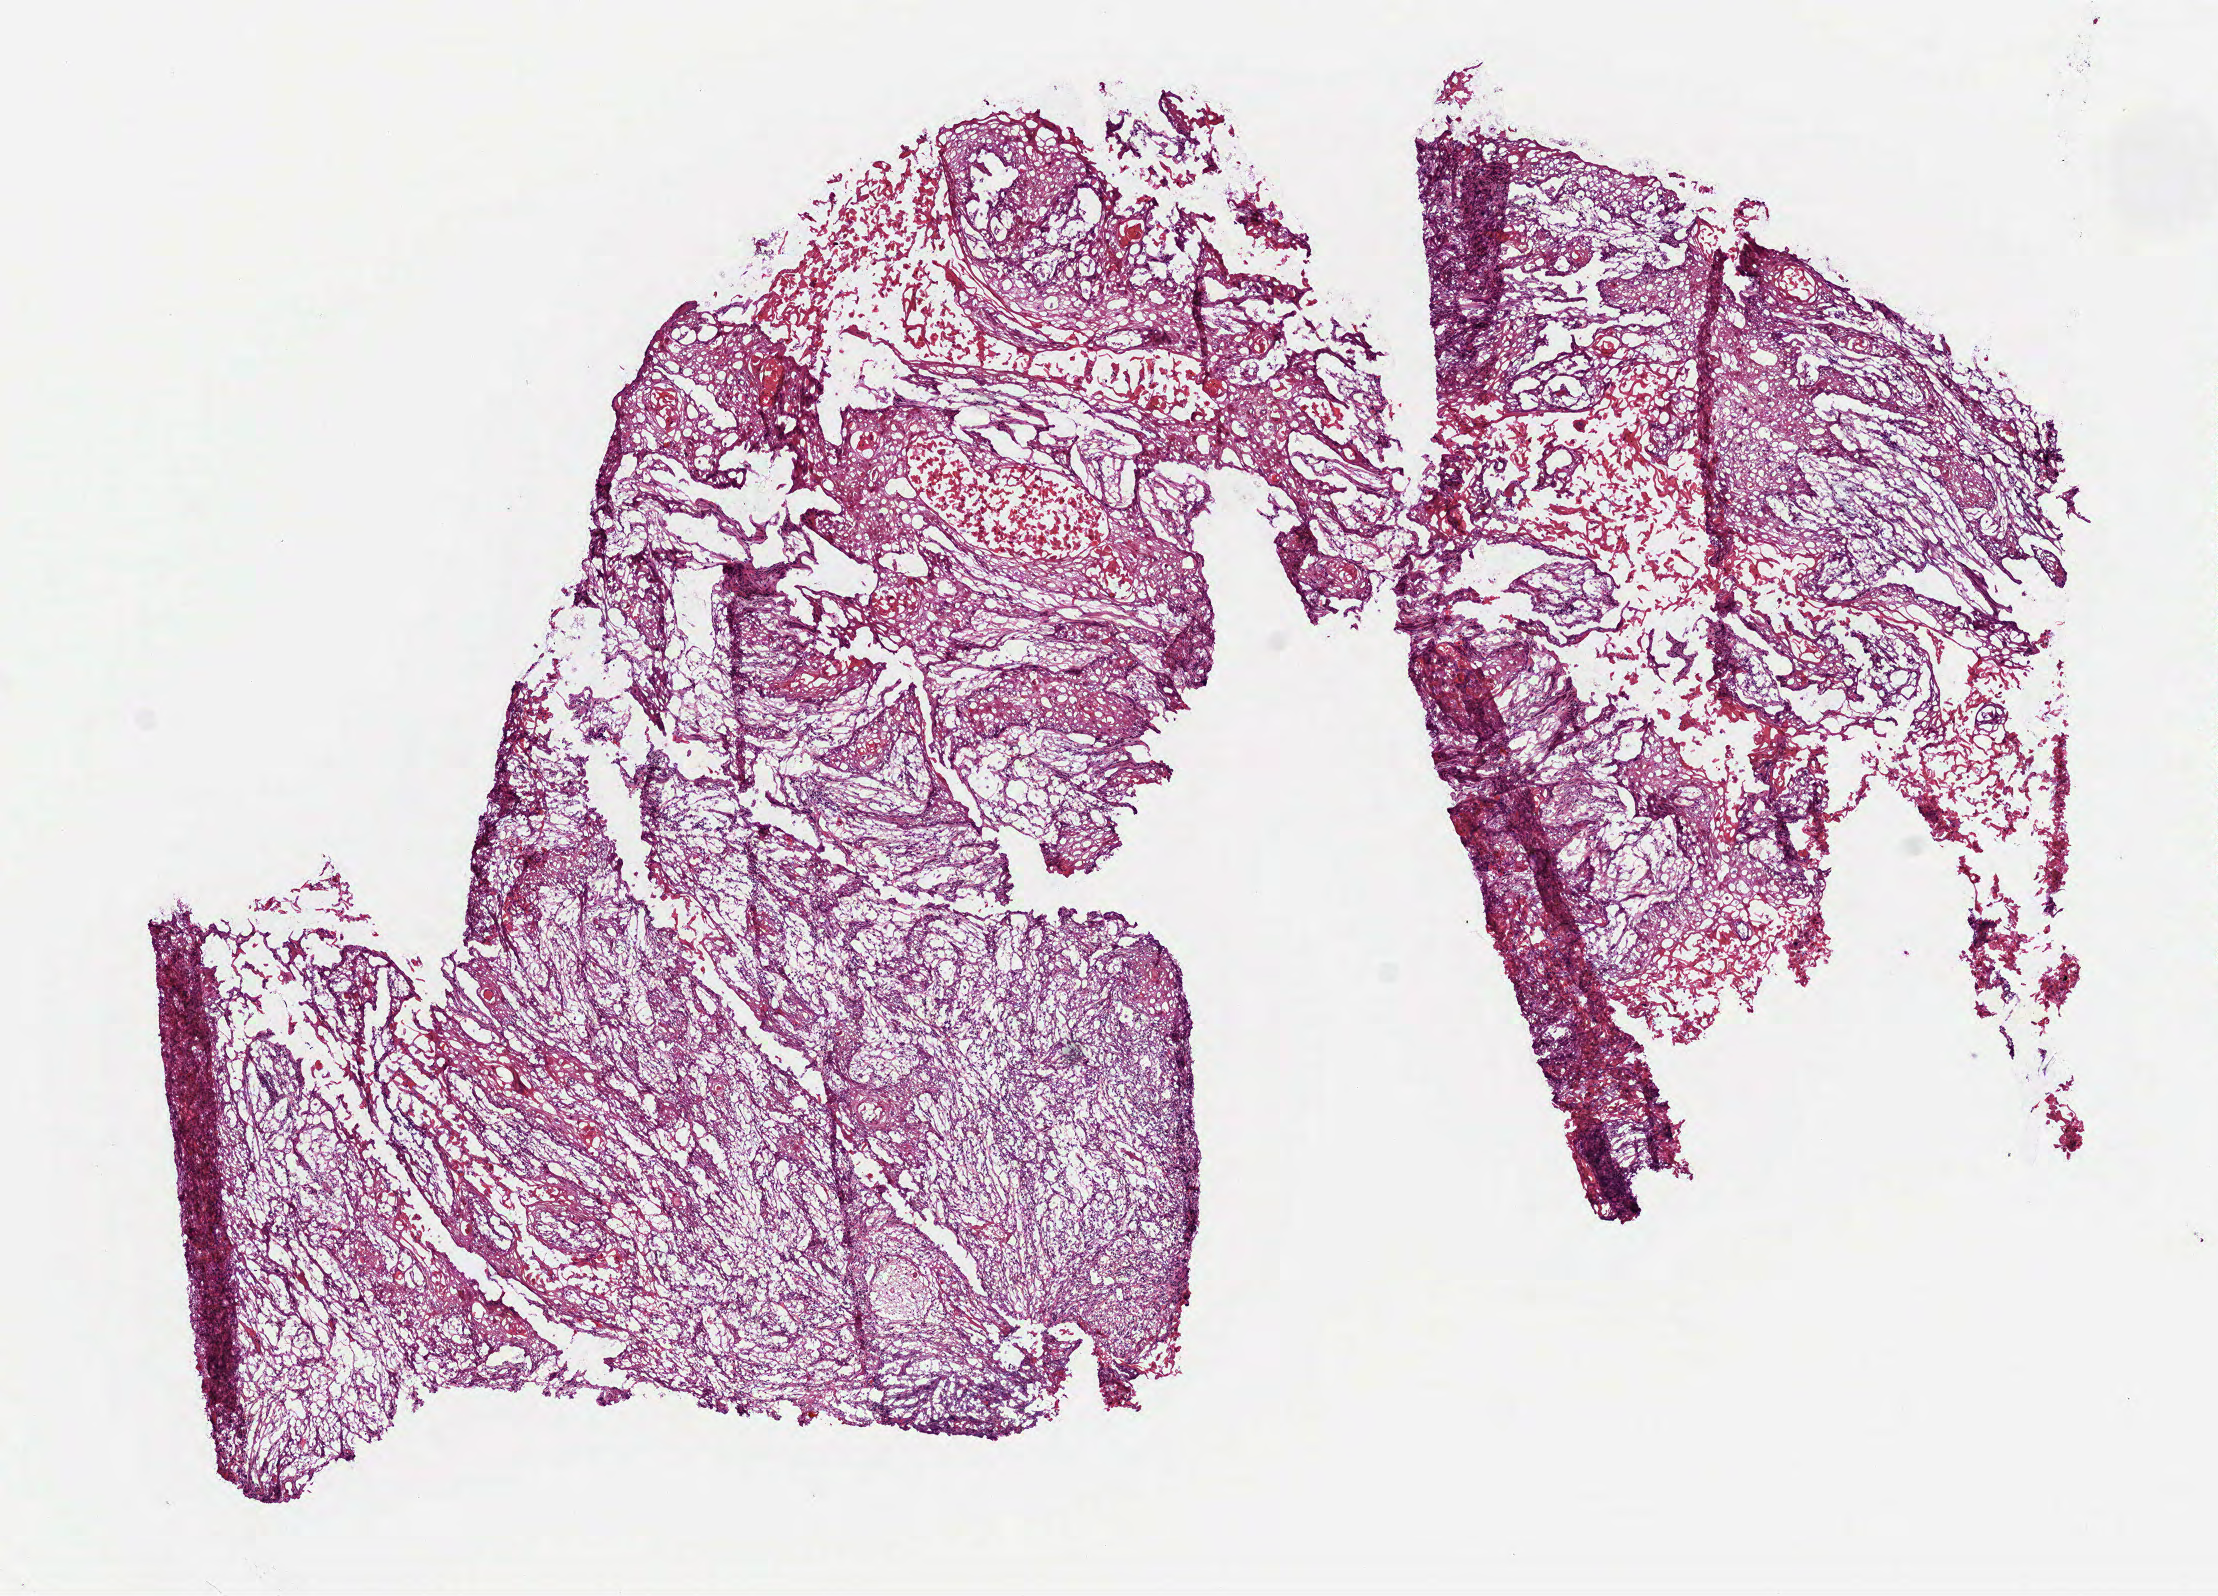
Digitized H&E tissue section (whole slide) — whole scanned area (about 8.9 x 6.4 mm, acquisition: 40x scan) shown as a low-resolution overview; frozen section; sample: primary tumour, head and neck. Patient: female, age at initial diagnosis 62 years. Histologic grade: G2 (moderately differentiated). Pathologist review of this section (percent, as recorded): tumour cells 60%, tumour nuclei 75%, normal cells 0%, stromal cells 40%, necrosis 0%.
Diagnosis: Squamous cell carcinoma, NOS. AJCC pathologic stage: IVA (7th edition).